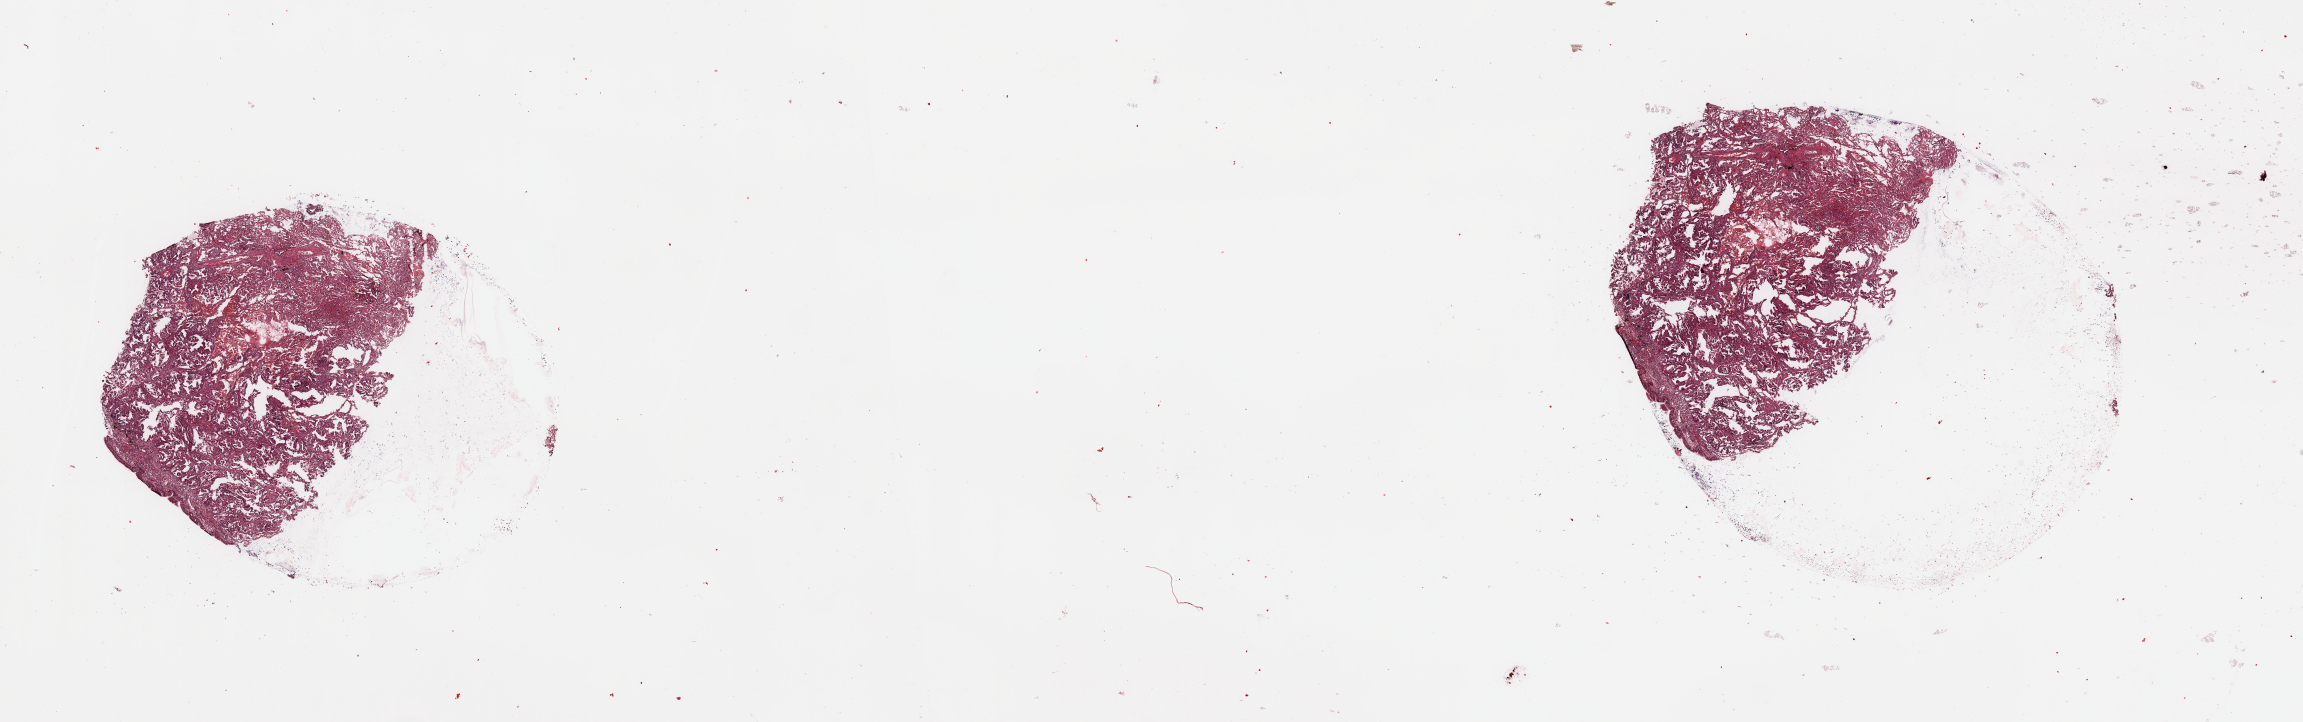
H&E-stained whole-slide image — whole scanned area (about 36.4 x 11.4 mm) shown as a low-resolution overview, lung, tumour tissue. Male, 59 y/o. Histologic grade: G2 (moderately differentiated).
* AJCC pathologic stage: IIIA
* diagnosis: Adenocarcinoma, NOS